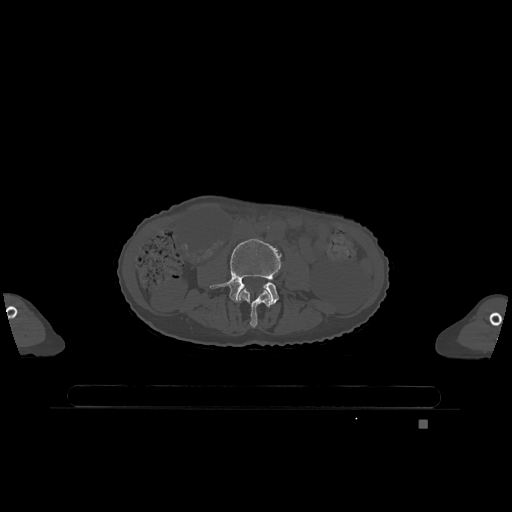
CT including the spine, one axial slice. Position 321 of 1317 along the scan axis. Bone window (W 1800 / L 400 HU). 0.5 mm slice thickness. 512 × 512 image matrix, field of view 500 × 500 mm. Patient: female, 74 years. From the clinical record (not read from this slice): primary cancer: lung; vertebrae with lytic lesions (as recorded): T1, T4, T5, T6, L4, L5.
Outlined on this slice (semi-automatically segmented with operator editing):
- L3 vertebra: box from (x=238, y=289) to (x=271, y=328) px
- L4 vertebra: (x=210, y=239)–(x=282, y=305)